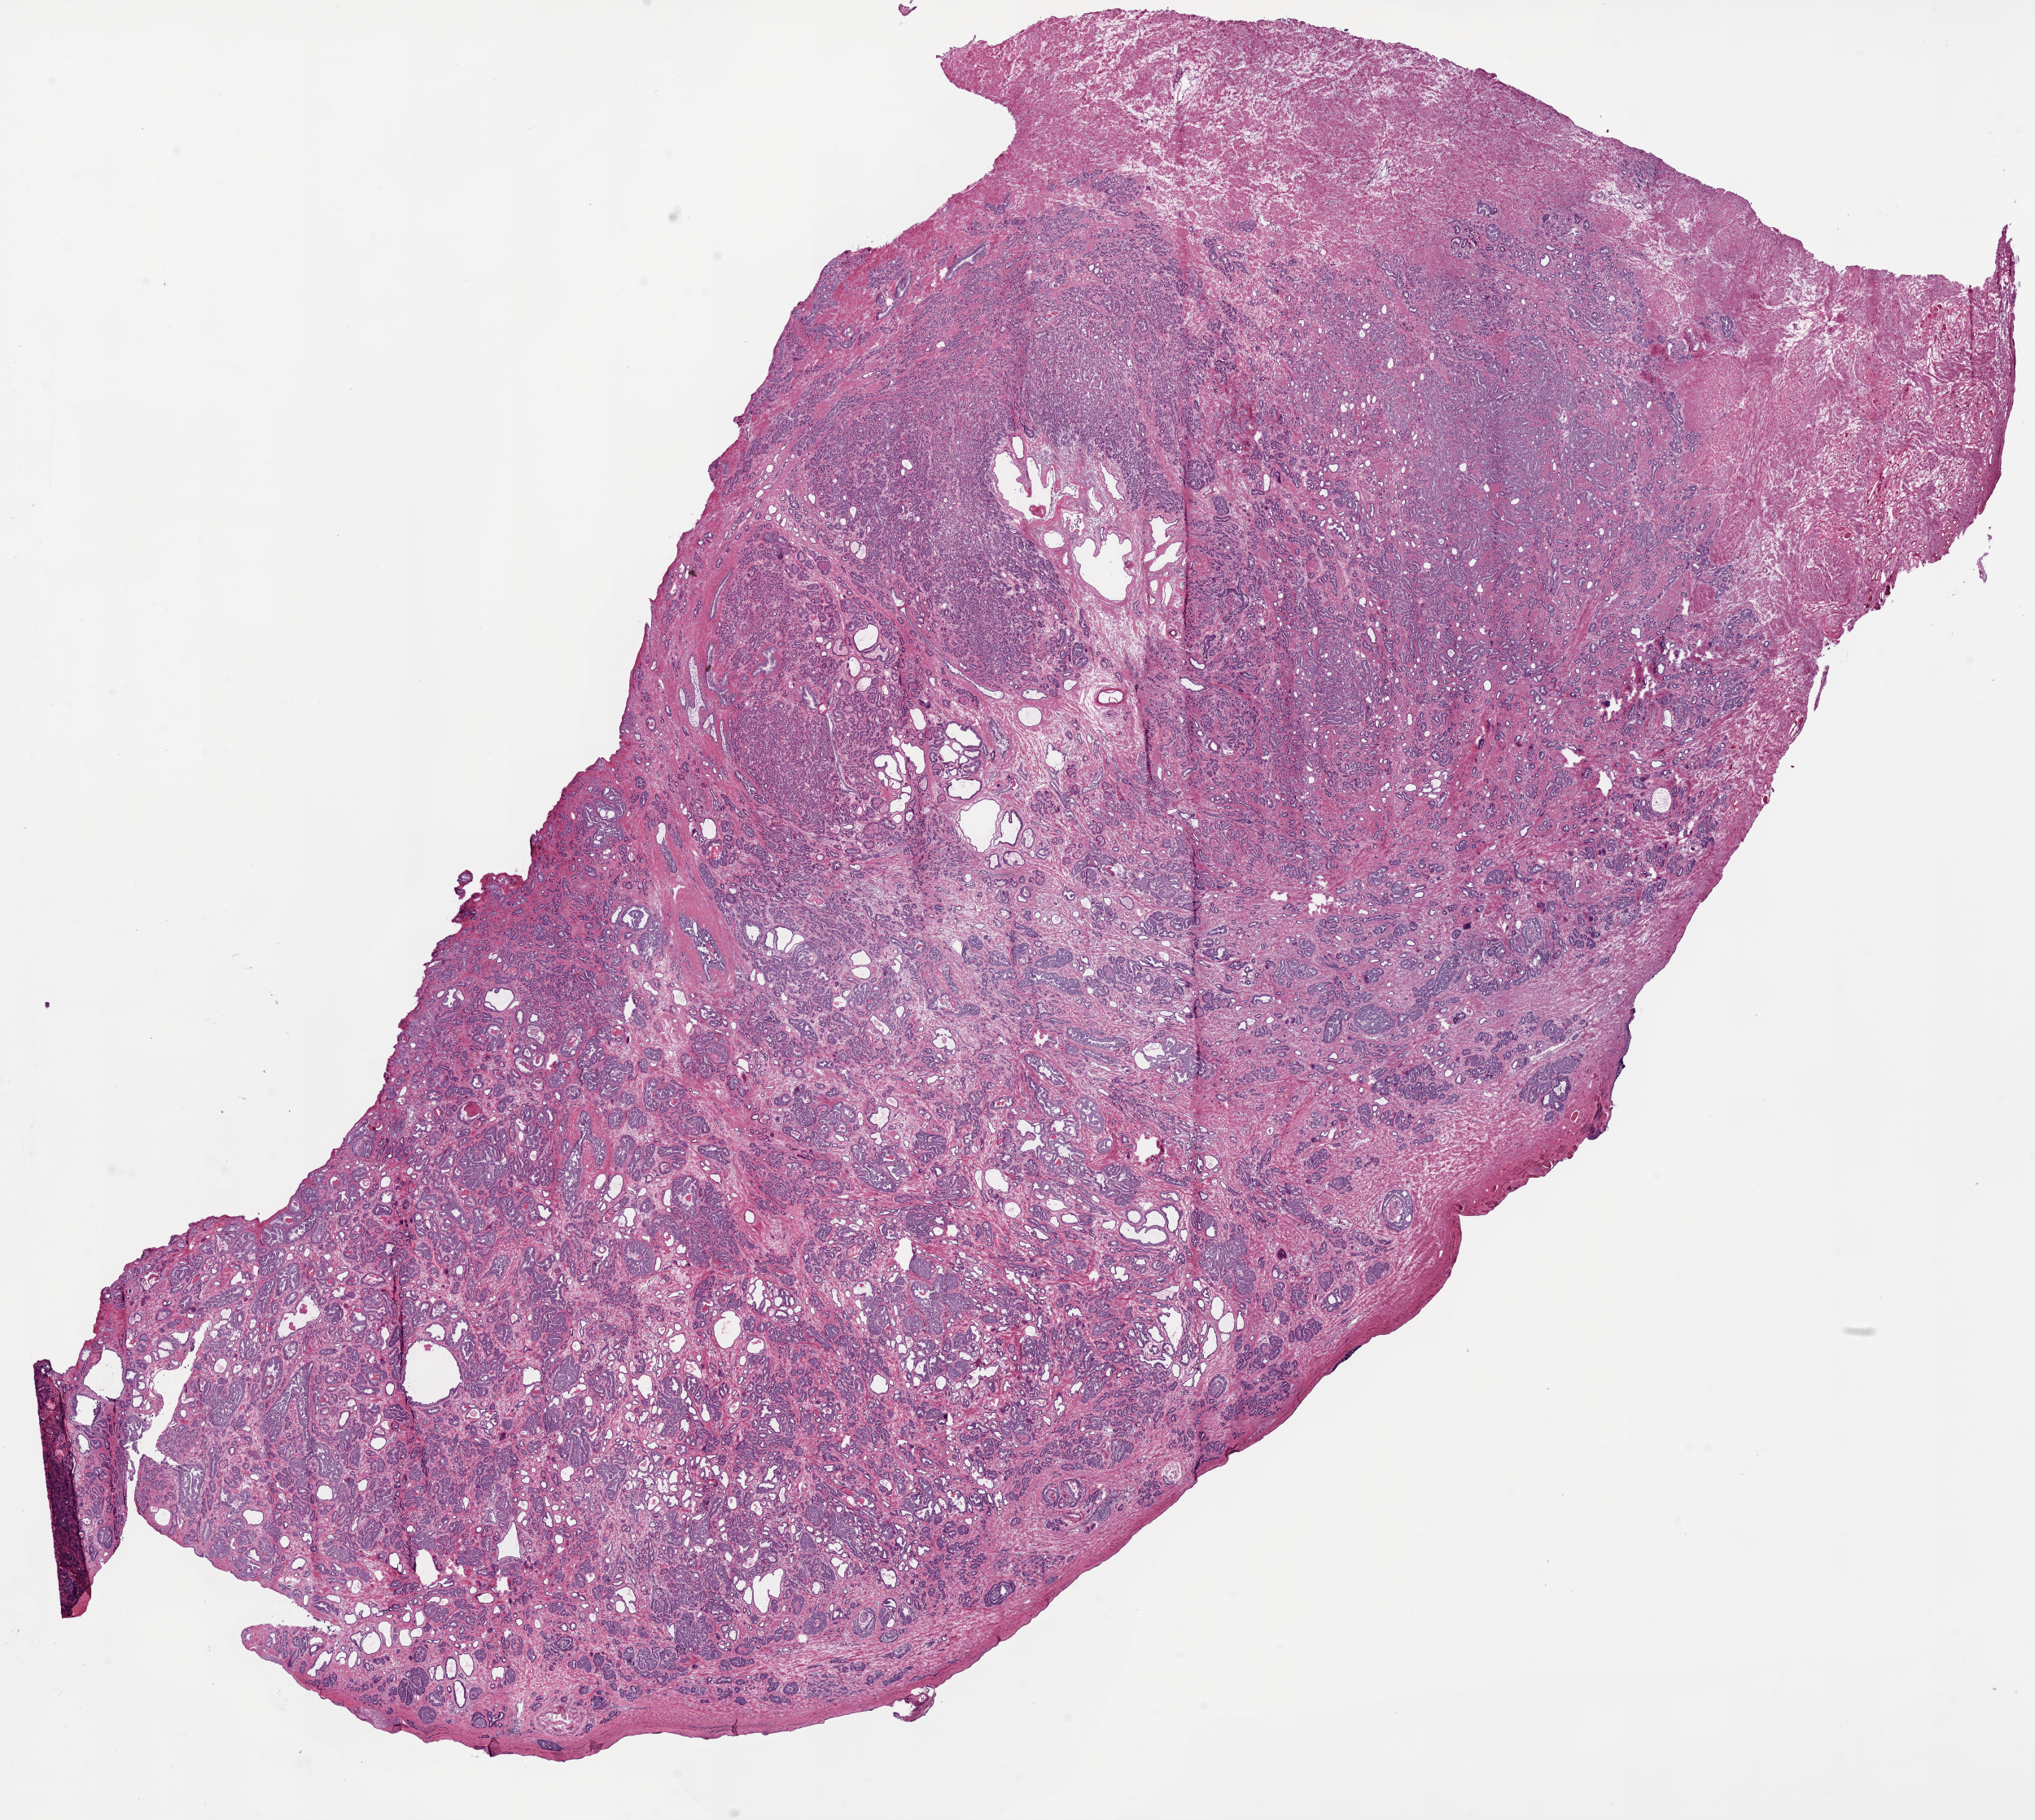
Whole-slide histology image, H&E, whole scanned area (about 20.1 x 17.9 mm) shown as a low-resolution overview, frozen section, primary tumour sample from the prostate. Patient: male, age at initial diagnosis 55 years. Gleason score: 7 (3+4). Pathologist review of this section (percent, as recorded): tumour cells 65%, tumour nuclei 70%, normal cells 15%, stromal cells 20%, necrosis 0%. Infiltration values recorded for this section: lymphocyte infiltration 1%, monocyte infiltration 0%, neutrophil infiltration 0%.
- diagnosis: Acinar cell carcinoma (prostate gland)